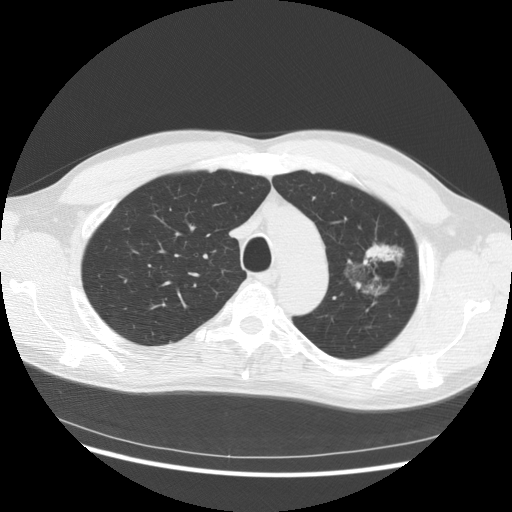
Chest CT (low-dose screening protocol), one axial image, third annual screen, lung window (W 1500 / L -600 HU), 512 × 512 image matrix. Male participant, aged 61 years at enrolment. Former smoker at enrolment.
Expert-annotated lung lesion, box from (x=332, y=235) to (x=408, y=315) px. The exam's reader record, not a measurement of the box and not confirmed to be the same lesion: non-calcified nodule or mass ≥4 mm, left upper lobe, 37 × 33 mm, poorly defined margins, mixed attenuation, pre-existing on the prior screen: yes; interval growth: yes. Official screen result: positive, other. Lung cancer was diagnosed 361 days after this screen: bronchiolo-alveolar adenocarcinoma, NOS, left upper lobe, well differentiated (G1), stage IB (AJCC 6th edition), 44 mm at pathology.